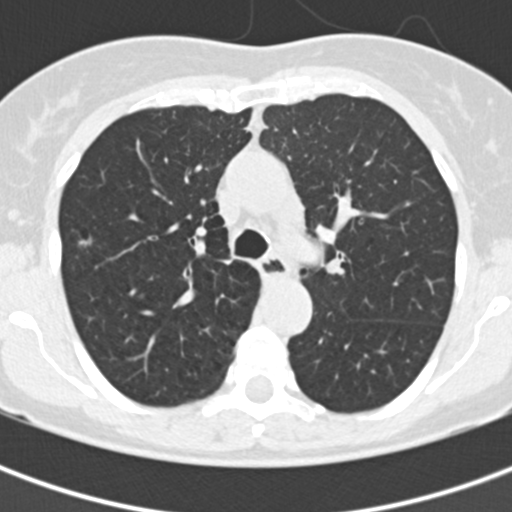
Low-dose screening chest CT, axial slice; baseline annual screen; lung window (W 1500 / L -600 HU); 2 mm slice thickness; 120 kVp; slice 64 of 177 in the series. Female participant, aged 60 years at enrolment.
Expert reader's lesion annotation, bounding box <58,221,110,268> (left, top, right, bottom; pixels). Screening reader's record for this exam: no non-calcified nodule ≥4 mm recorded. Official screen result: negative screen, no significant abnormalities. Lung cancer was diagnosed 861 days after this screen (after the third annual screen): bronchiolo-alveolar adenocarcinoma, NOS, right upper lobe, well differentiated (G1), stage IA (AJCC 6th edition), 11 mm at pathology.